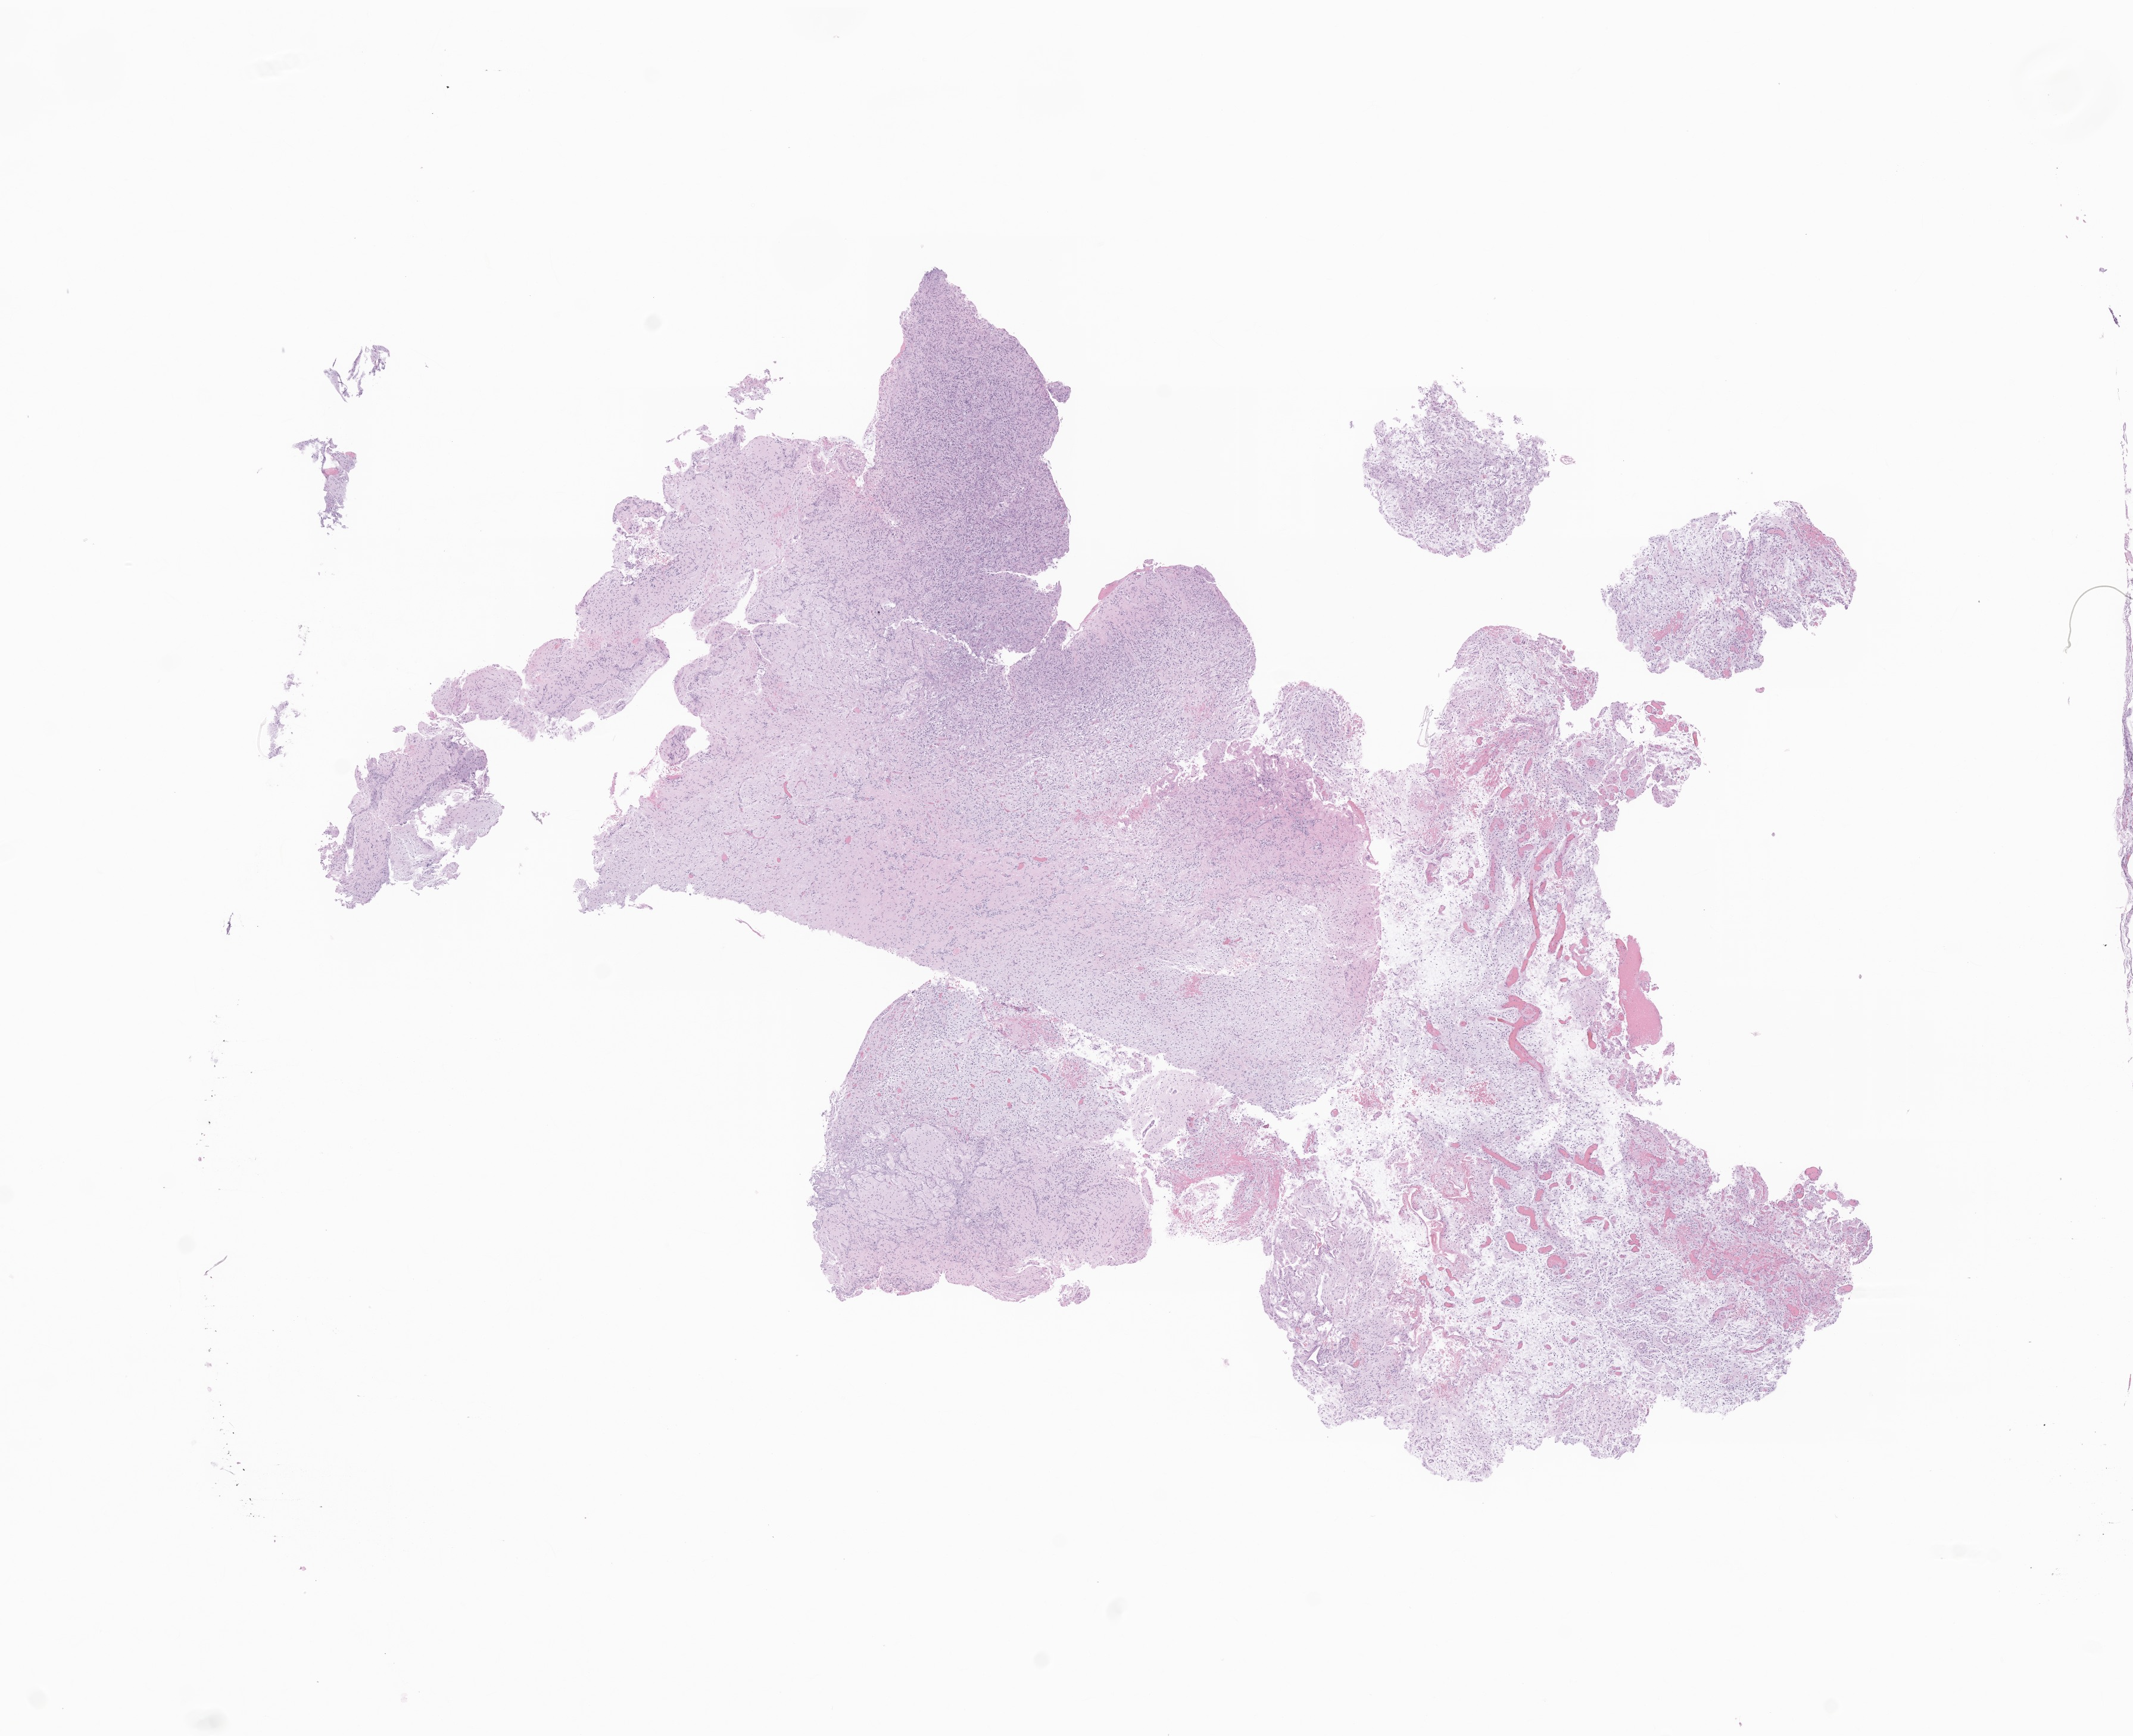
Whole-slide image, hematoxylin and eosin (H&E) stain of tumor tissue from the cerebellum — shown as a low-resolution overview of the whole scanned area (about 15.1 x 12.3 mm). Formalin-fixed paraffin-embedded section. Female patient, age 166 months (13 years 10 months).
Diagnosis (ICD-O-3 morphology term): Astrocytoma, NOS.